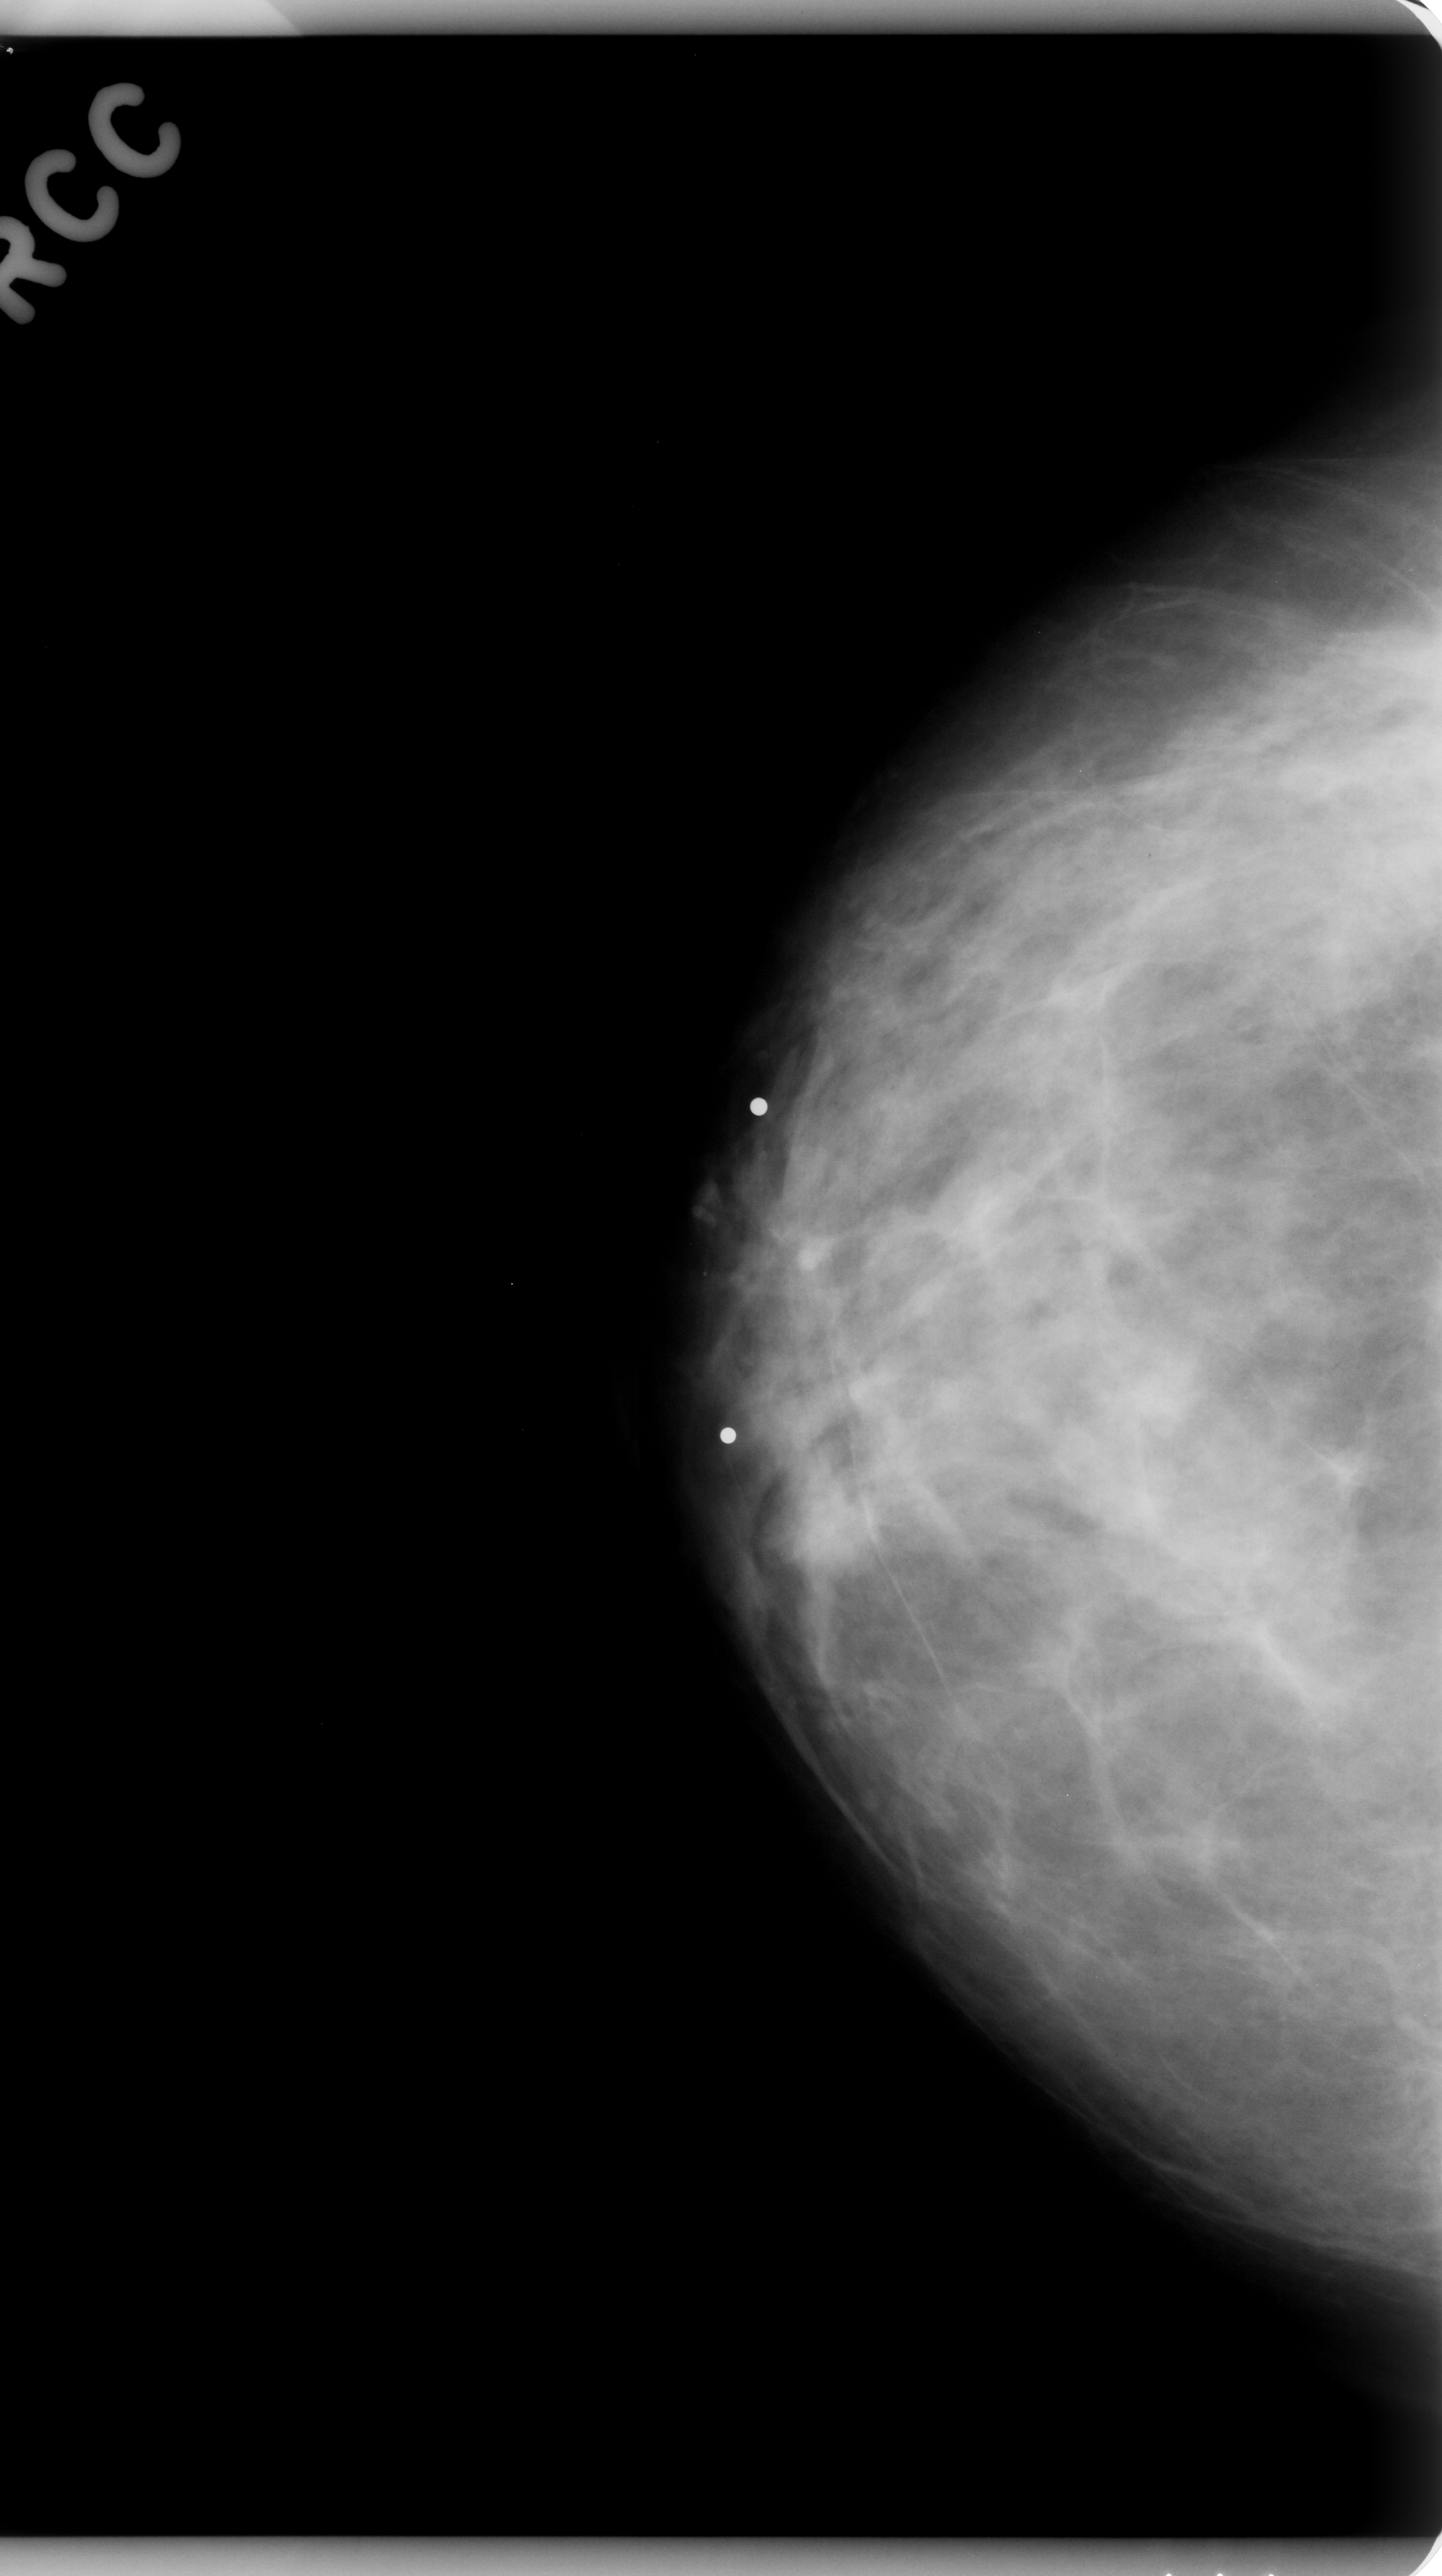
Scanned film-screen mammogram; right breast; craniocaudal (CC) view.
Abnormality record for this image: mass, shape oval, margins microlobulated; BI-RADS assessment category 4; pathology (as recorded): benign.